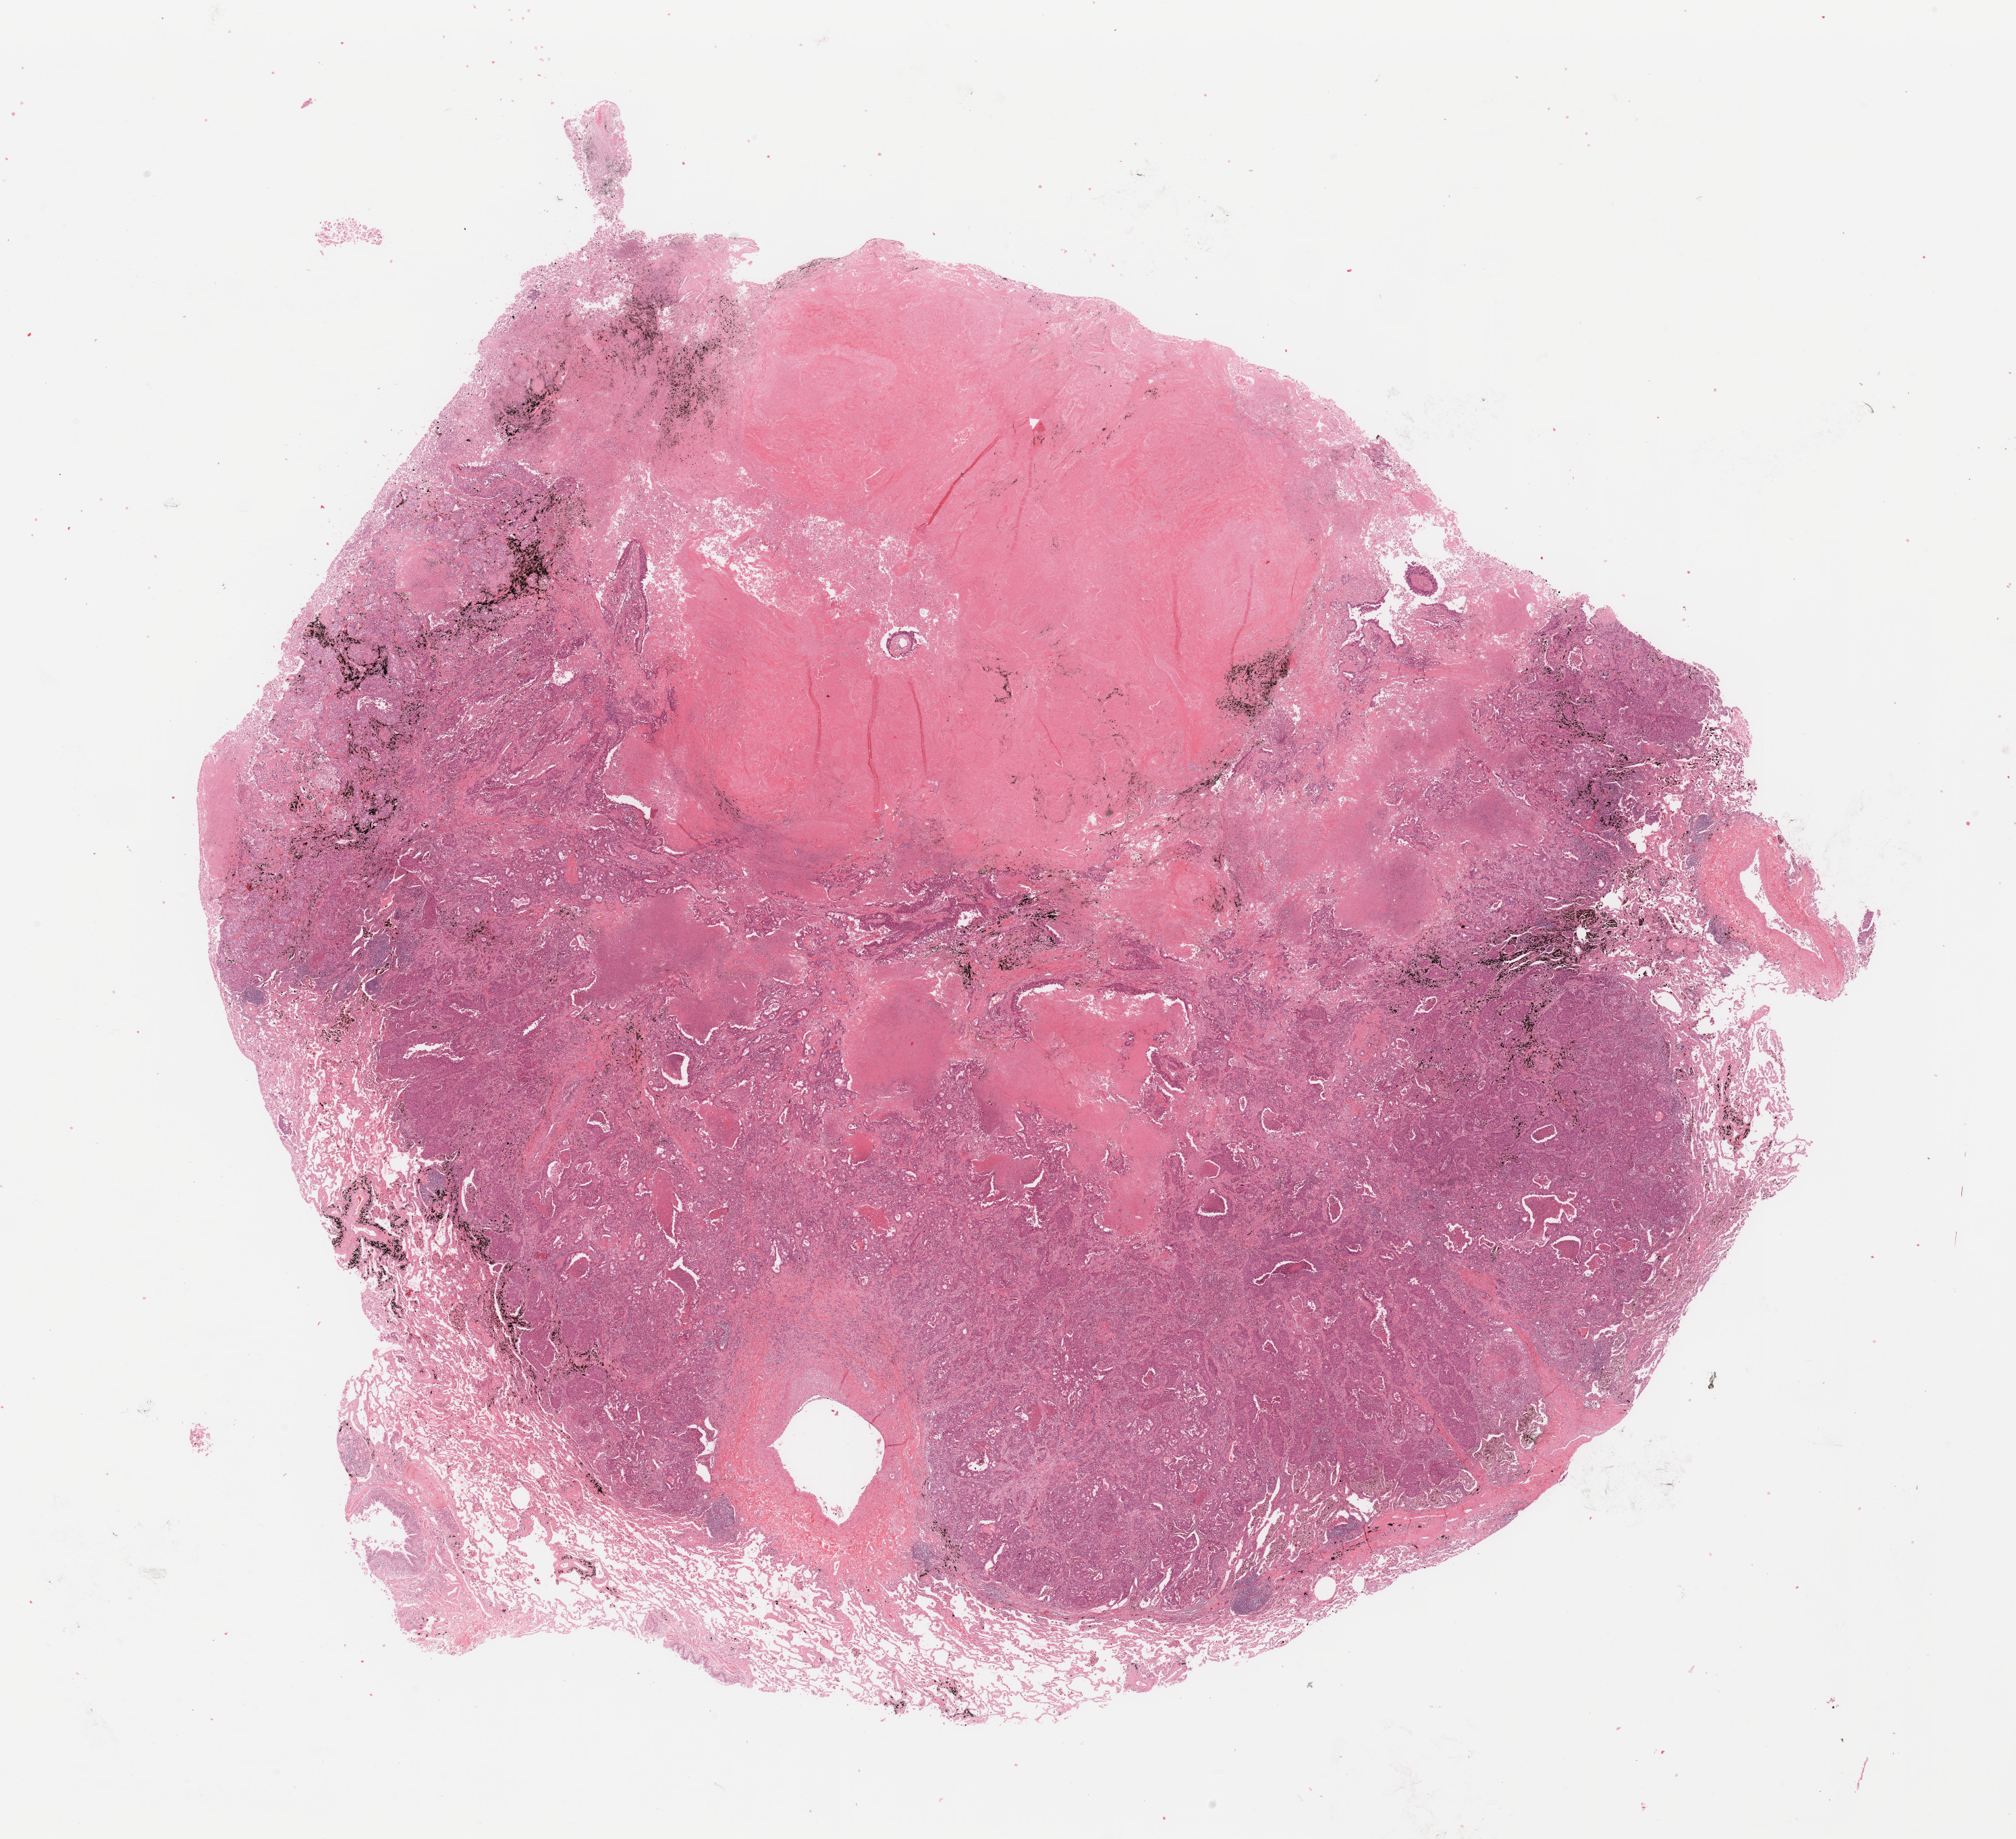
Digitized H&E tissue section (whole slide) — shown as a low-resolution overview of the whole scanned area (about 23.6 x 21.6 mm, from a 20x scan), tumour tissue sample, lung. Male, 64 y/o.
* patient diagnosis (cohort enrolment): squamous cell carcinoma (lung)